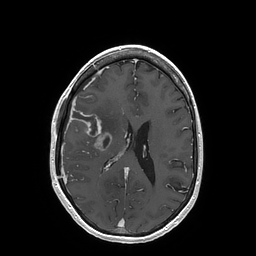
Brain MRI from a brain-tumour surgery series, one axial slice; slice 71 of 202 in the series (ordered by position); T1-weighted post-contrast; 256 × 256 image matrix. Case-level facts recorded for this patient, not image findings: histopathology: Glioblastoma; WHO grade: 4; IDH mutation: no; tumour location: Right Insular.
Annotated regions visible in this slice (outlined manually by an expert reader):
- tumour: bounding box <70,108,111,151> (left, top, right, bottom; pixels)